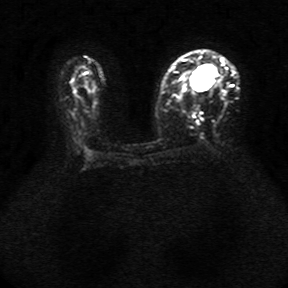
Breast MRI, one axial slice; diffusion-weighted series; image 2 of 4 stored at this slice position (different b-values; order by instance number); 1.5 T; 5 mm slice thickness; 288 × 288 image matrix. Female patient.
Outlined on this slice (manually delineated by an expert):
- tumour on diffusion-weighted imaging: box from (x=191, y=70) to (x=213, y=91) px